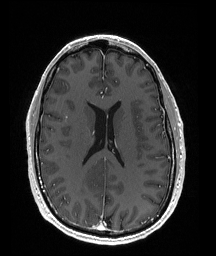
Brain MRI from a brain-tumour surgery series, one axial slice; slice 77 of 176 in the series (ordered by position); T1-weighted post-contrast; 1 mm slice thickness; 216 × 256 image matrix, field of view 211 × 250 mm. From the clinical record (not read from this slice): histopathology: Oligodendroglioma; WHO grade: 2; IDH mutation: yes; tumour location: Right Parietal.
Outlined on this slice (outlined manually by an expert reader):
- tumour: bounding box [x1, y1, x2, y2] px = [78, 165, 97, 194]